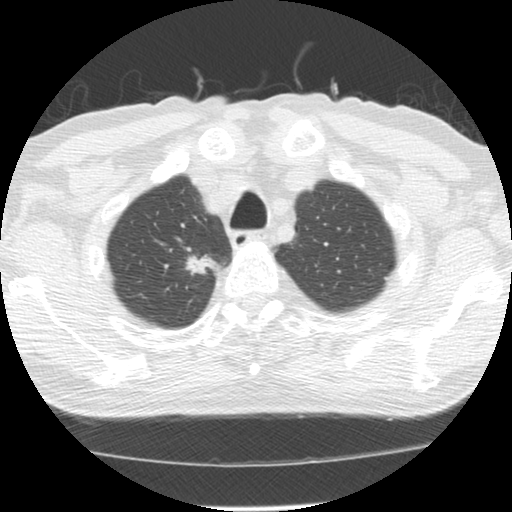
Low-dose screening chest CT, one axial slice; position 115 of 139 along the scan axis; reconstruction kernel STANDARD; lung window (W 1500 / L -600 HU); 512 × 512 image matrix.
Structures marked on this image (manually delineated by an expert):
- lesion 1 (tumor, upper lobe of right lung): box from (x=187, y=254) to (x=221, y=276) px